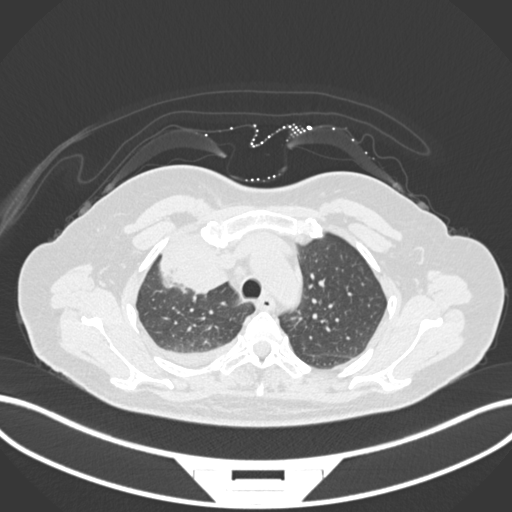
Chest CT, one axial slice. Slice 125 of 172 in the series (ordered by position). Reconstruction kernel B30f. 120 kVp. Lung window (W 1500 / L -600 HU). 512 × 512 image matrix, field of view 400 × 400 mm. Patient: female, 52 years. From the clinical record (not read from this slice): clinical TNM (as recorded): T3 N1 M1.
Outlined on this slice (rectangle marked by the reading radiologist):
- lung tumour (recorded histology: adenocarcinoma): bounding box <158,226,230,292> (left, top, right, bottom; pixels)